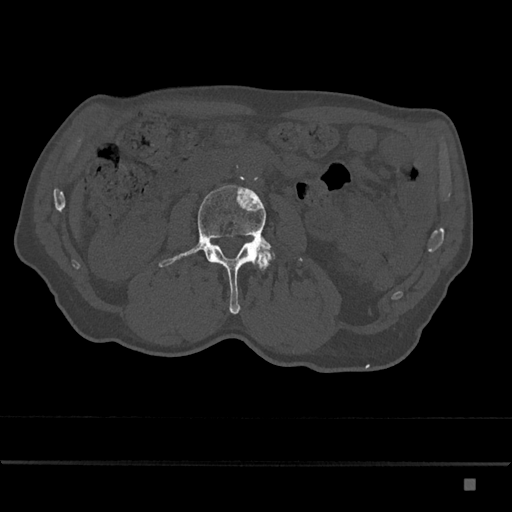
CT including the spine, one axial slice; slice 405 of 797 in the series (ordered by position); 120 kVp; bone window (W 1800 / L 400 HU); 0.5 mm slice thickness; 512 × 512 image matrix, field of view 390 × 390 mm. Patient: male, 72 years. Case-level facts recorded for this patient, not image findings: primary cancer: prostate.
Structures marked on this image (semi-automatic segmentation, software-assisted and operator-edited):
- L3 vertebra: bounding box <158,185,303,314> (left, top, right, bottom; pixels)
- L4 vertebra: <257,250,274,271>